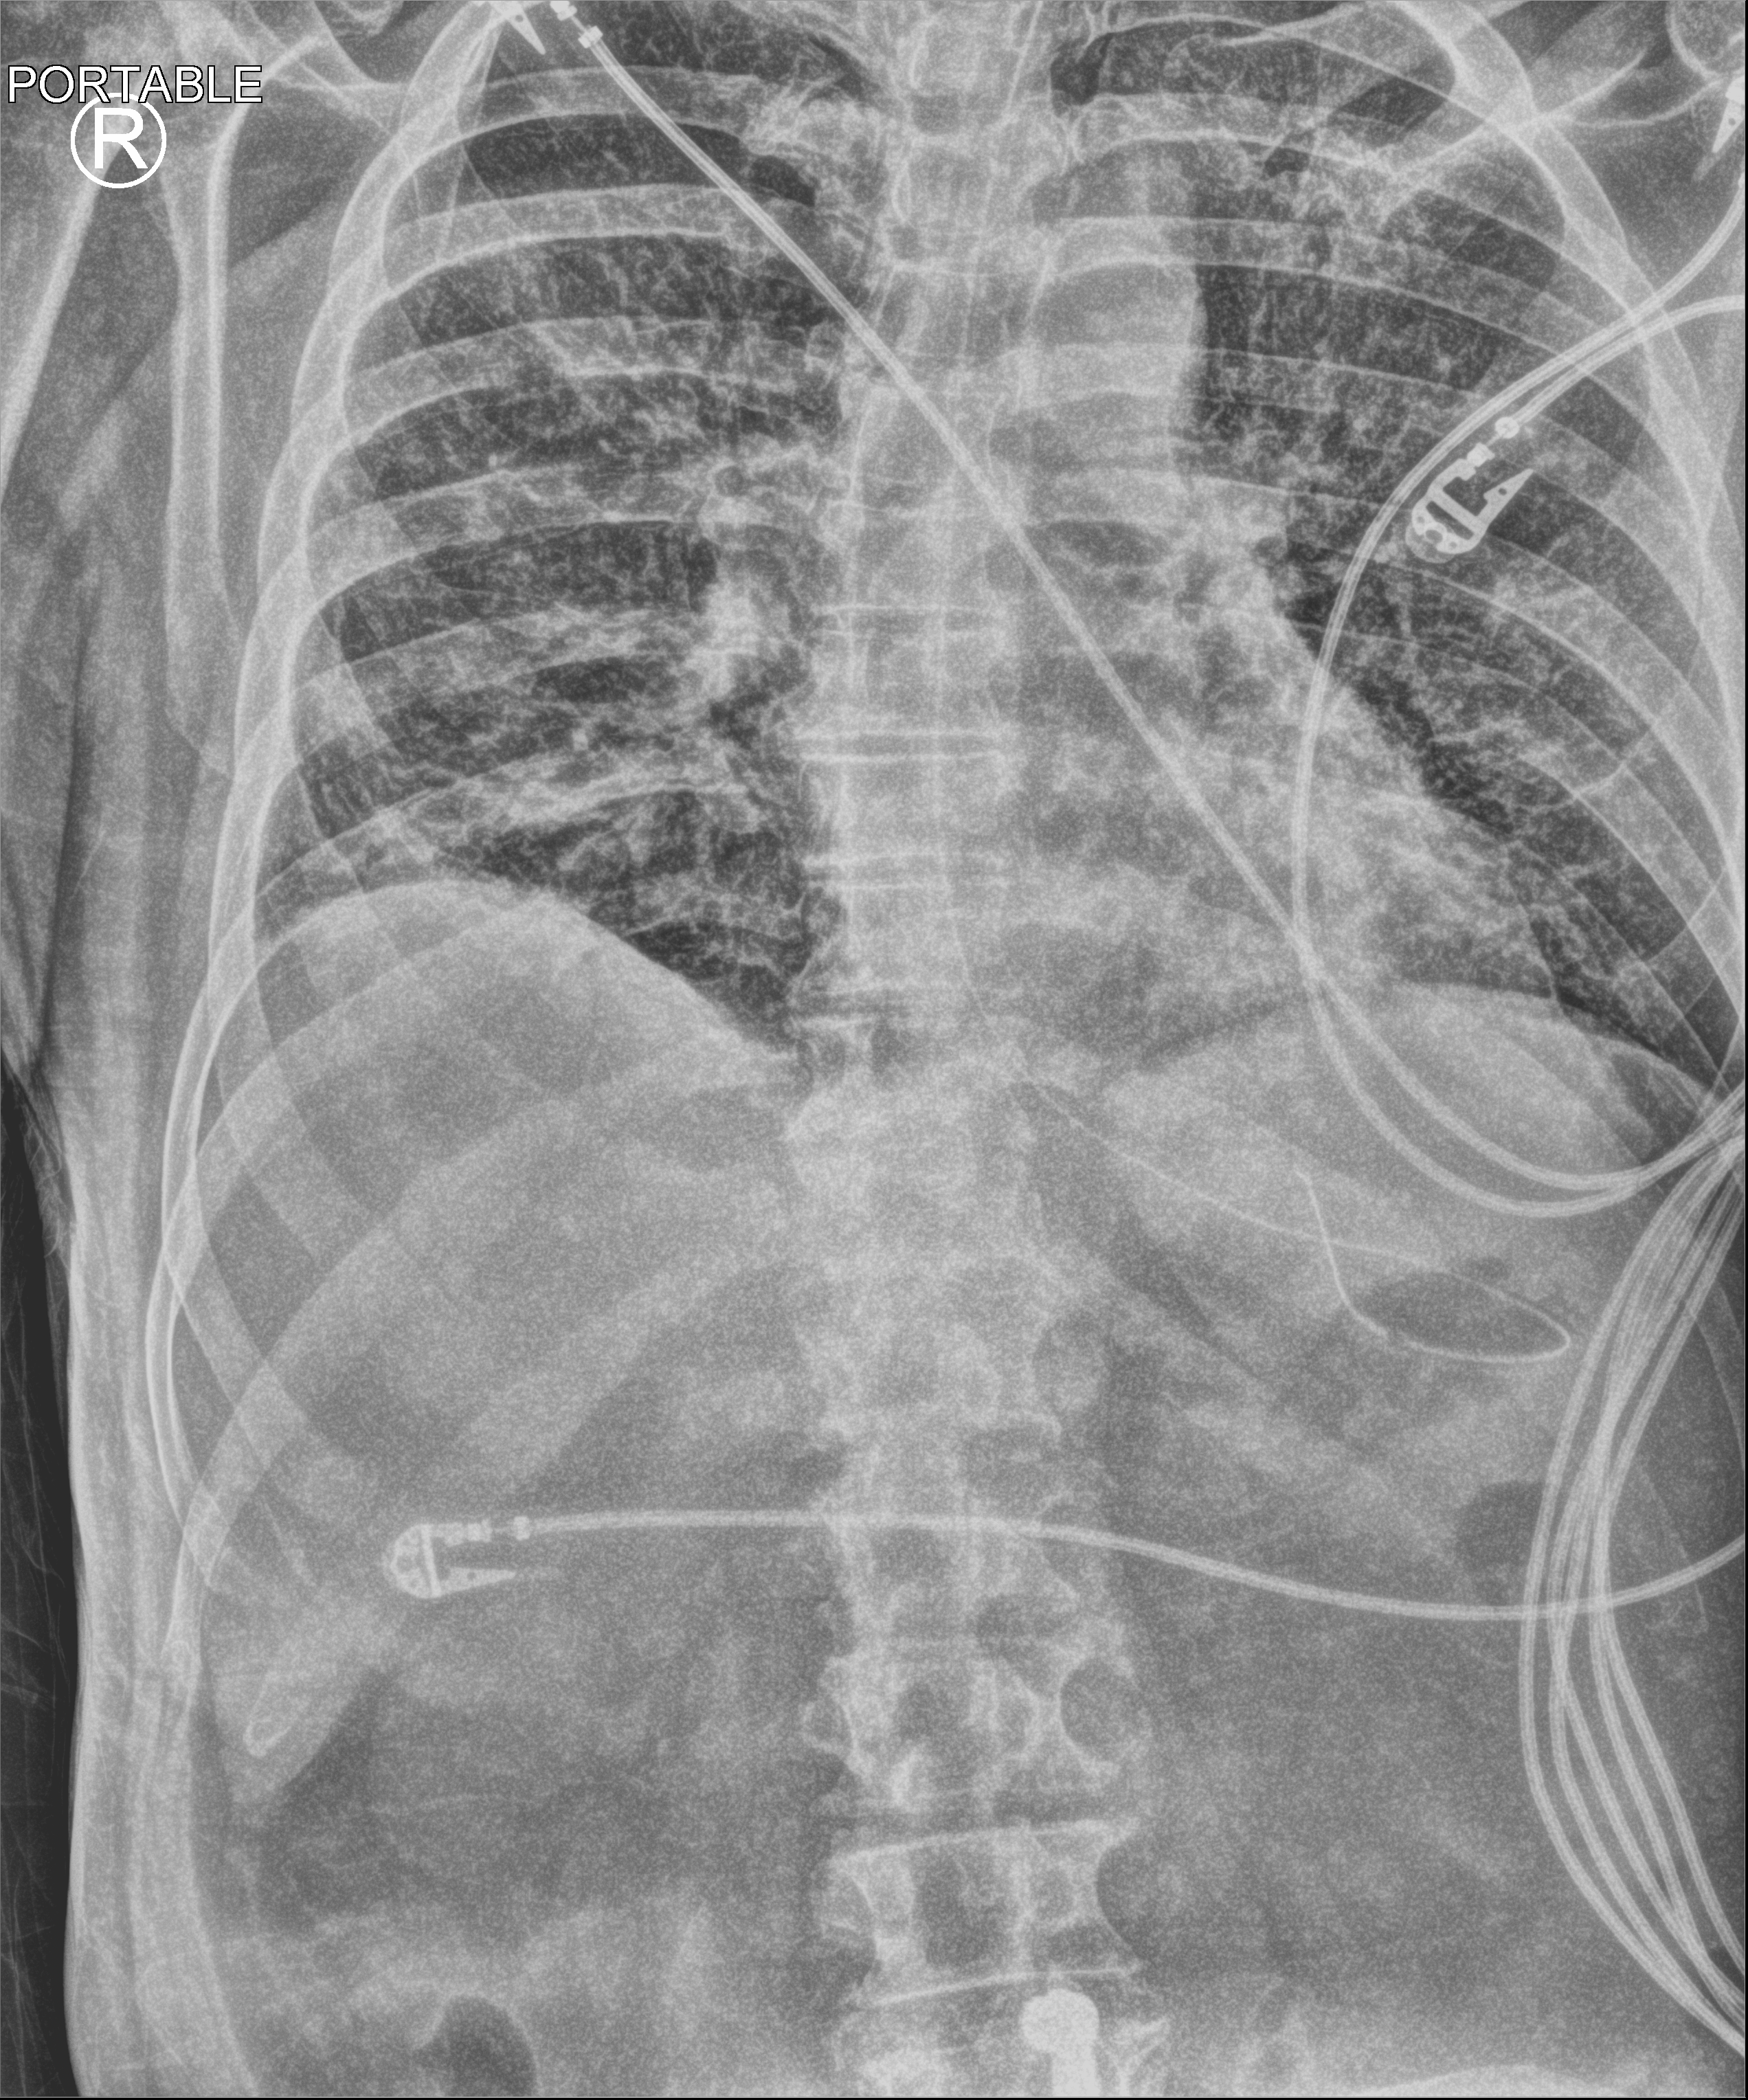
Chest X-ray (portable), anteroposterior (AP) projection. Patient hospitalised with COVID-19; male, aged 60–74 years.
Admission-level facts for this patient (not findings on this image; timing relative to this image not recorded): admitted to intensive care during this hospital stay: yes; mechanically ventilated during this hospital stay: yes.